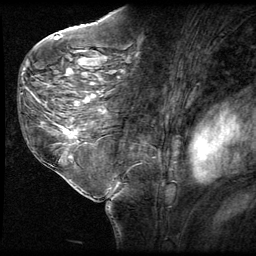
Breast MRI (dynamic contrast-enhanced), one sagittal slice; 3 images stored at this slice position (order not interpretable as contrast timing); 1.5 T; TE 4.2 ms, TR 9 ms; 2.5 mm slice thickness; 256 × 256 image matrix, field of view 180 × 180 mm. Patient: female, 58 years. Case-level facts recorded for this patient, not image findings: setting: breast cancer imaged before/during neoadjuvant chemotherapy; receptor status: HR-positive, HER2-negative.
Structures marked on this image (semi-automatic segmentation, software-assisted and operator-edited):
- analysis volume of interest (the breast-tissue region the enhancement analysis was run in; not a lesion): box from (x=51, y=116) to (x=93, y=151) px
- tumour enhancement mask (voxels above the 140 % enhancement threshold inside the analysis volume of interest): (x=68, y=130)–(x=77, y=139)